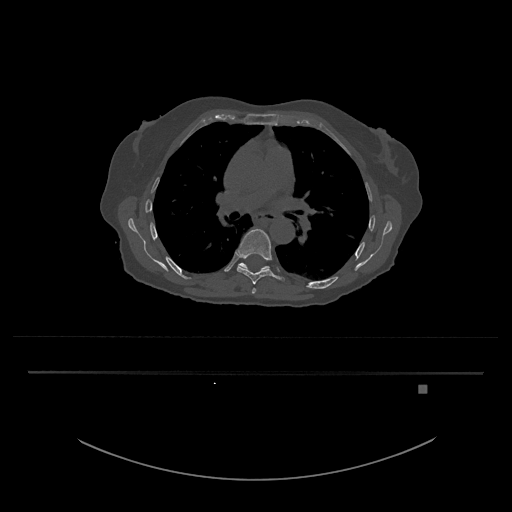
CT including the spine, one axial slice; slice 797 of 797 in the series (ordered by position); reconstruction kernel Br40s/3; bone window (W 1800 / L 400 HU); 0.5 mm slice thickness; 512 × 512 image matrix, field of view 500 × 500 mm. Patient: female, 57 years. Case-level facts recorded for this patient, not image findings: primary cancer: cervical.
Structures marked on this image (semi-automatic segmentation, software-assisted and operator-edited):
- T8 vertebra: bounding box (x1, y1, x2, y2) in pixels: (235, 229, 285, 285)
- T9 vertebra: (239, 259, 271, 271)